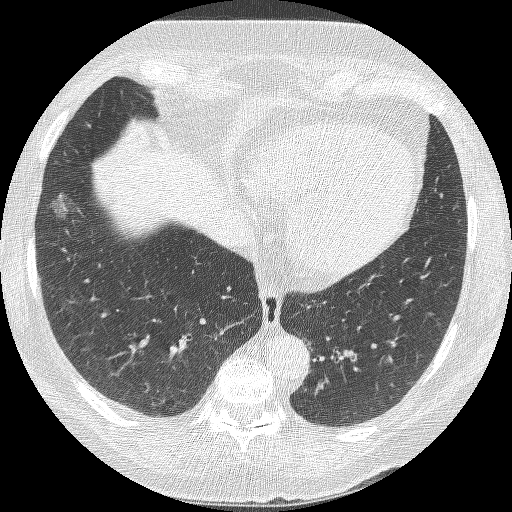
Low-dose screening chest CT, axial slice; second annual screen; lung window (W 1500 / L -600 HU); 1.25 mm slice thickness; lung (sharp) reconstruction kernel (BONE); slice 88 of 245 in the series; 512 × 512 image matrix, field of view 310 × 310 mm. Female, age 68 years at enrolment. Current smoker at enrolment.
Lesion marked by an expert reader, box from (x=35, y=190) to (x=78, y=241) px. Screening reader's record for this exam (one nodule recorded; not confirmed to be the boxed lesion): non-calcified nodule or mass ≥4 mm, right lower lobe, 18 × 15 mm, poorly defined margins, ground glass attenuation, pre-existing on the prior screen: yes; interval growth: yes. Participant outcome: lung cancer diagnosed 42 days after this screen — bronchiolo-alveolar adenocarcinoma, NOS, right lower lobe, well differentiated (G1), stage IA (AJCC 6th edition), 13 mm at pathology.